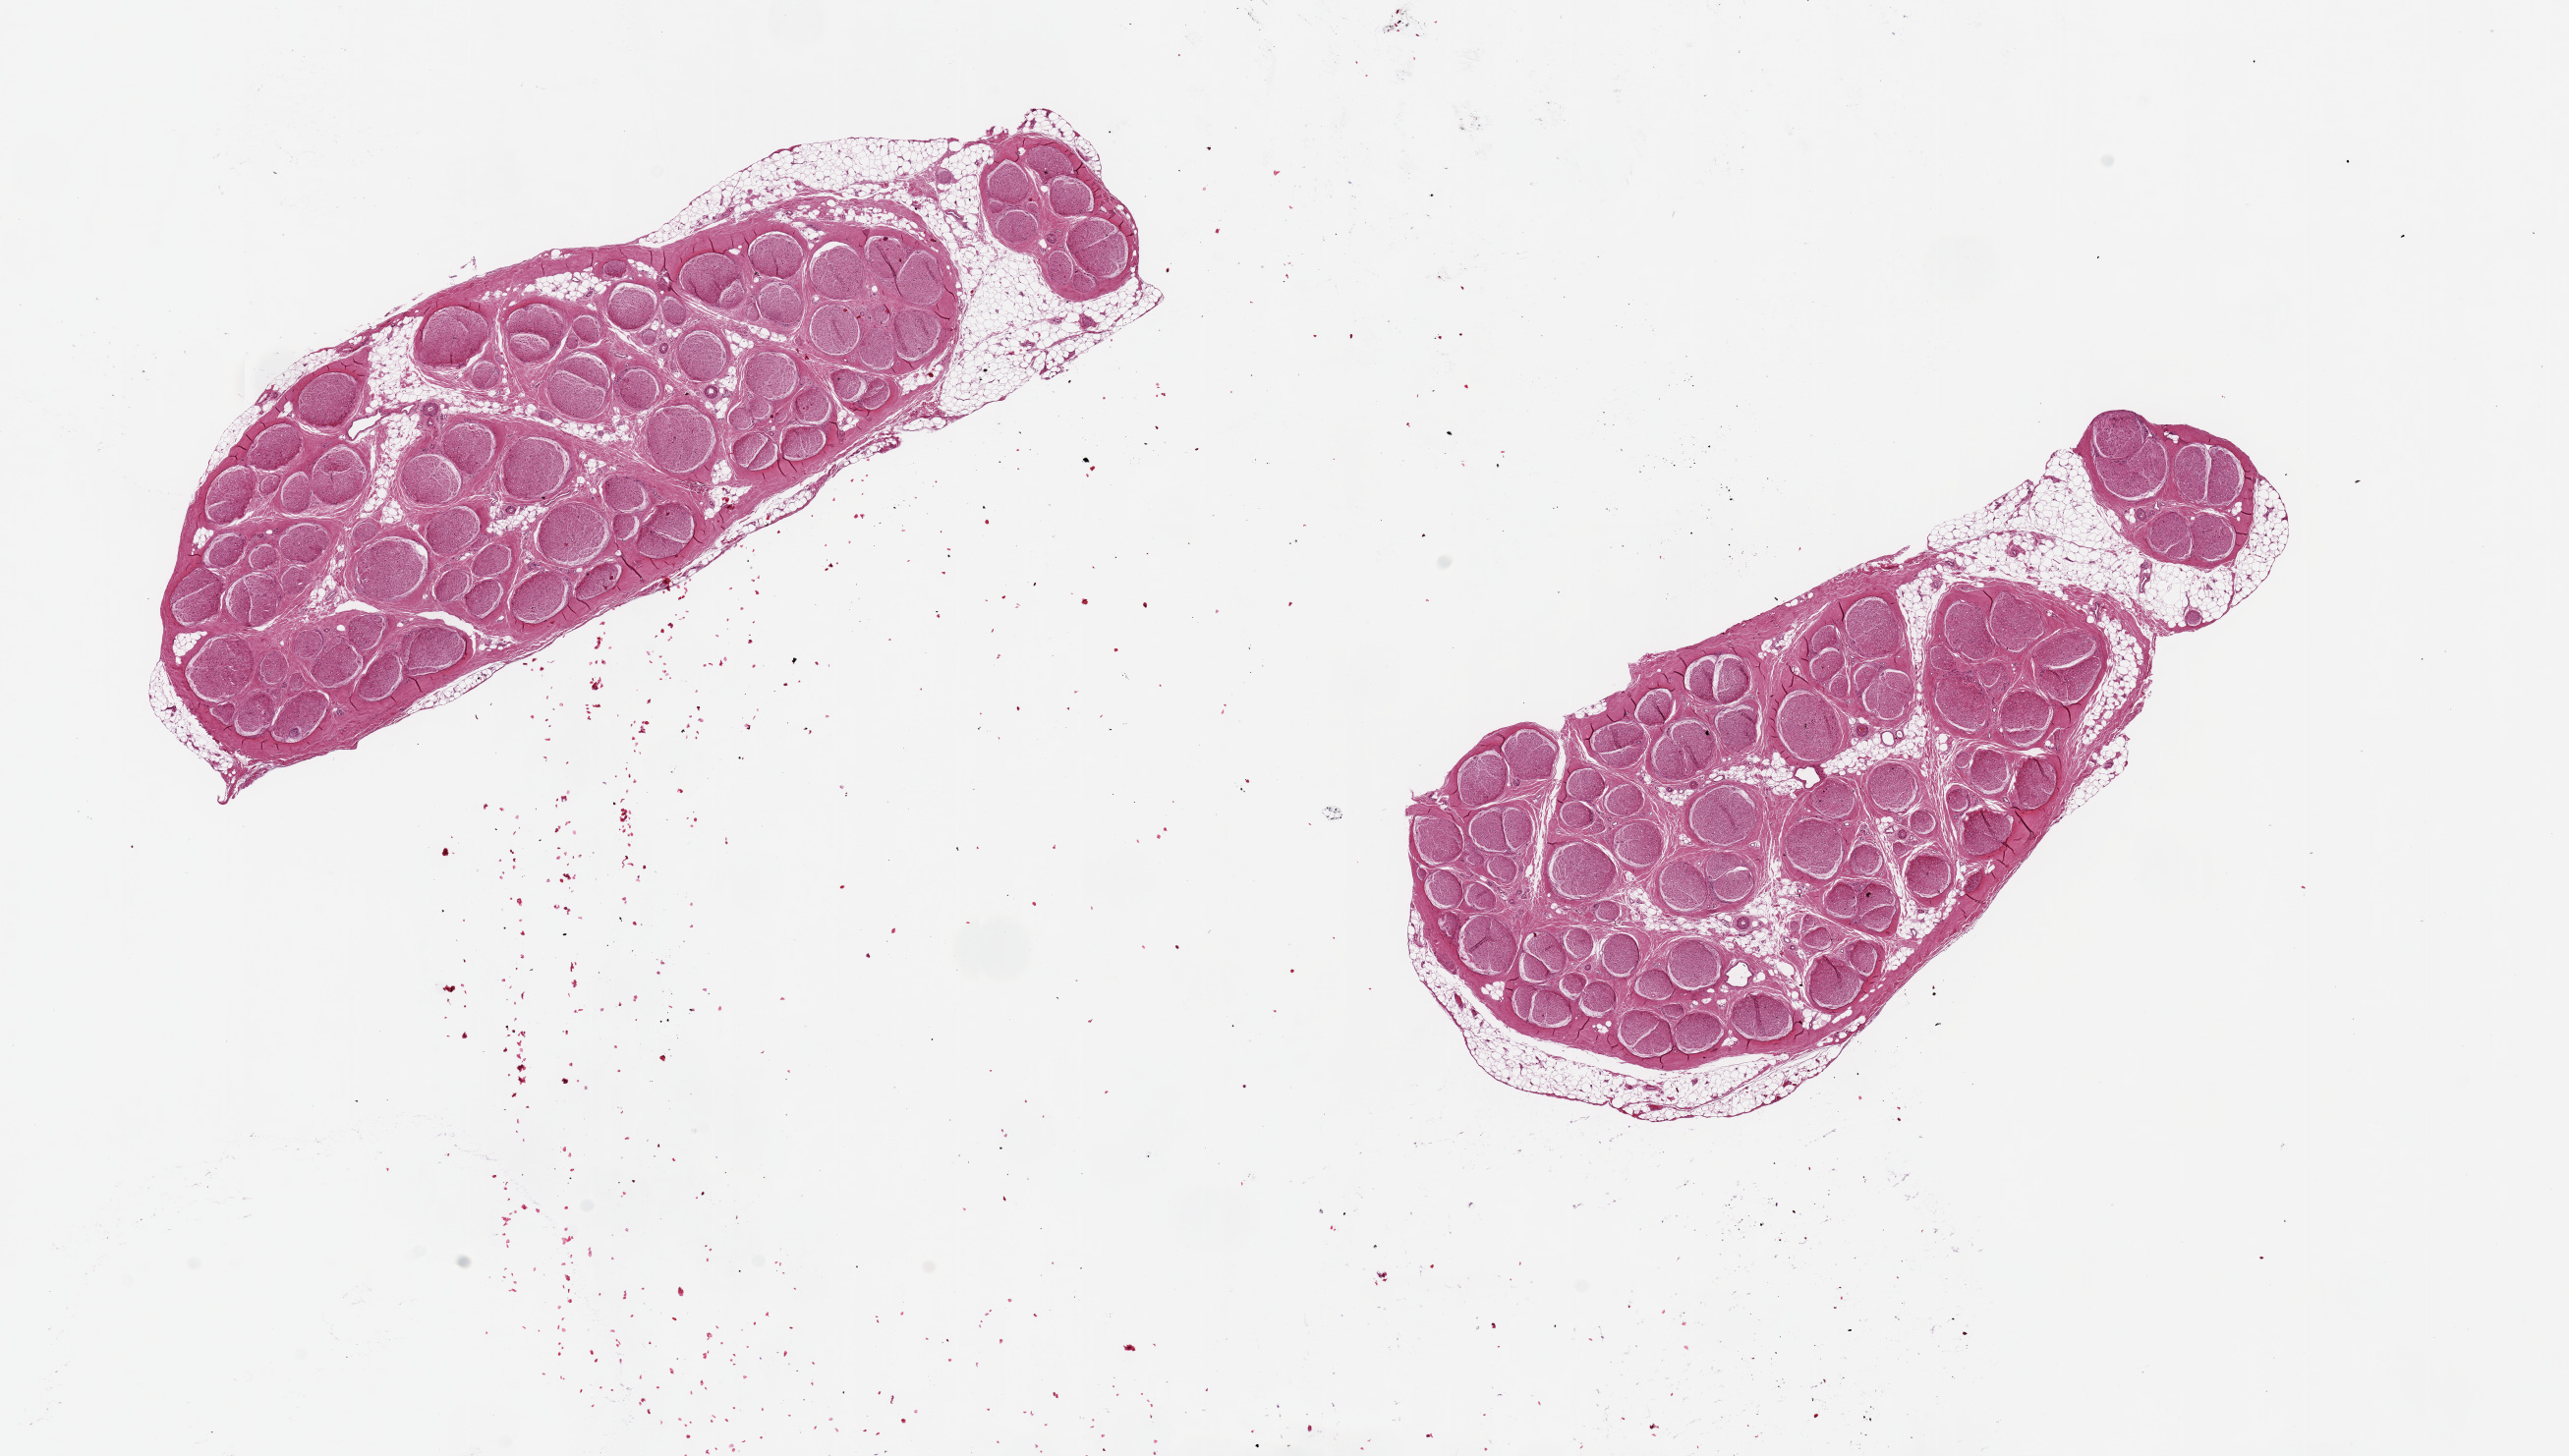
Digitized hematoxylin and eosin (H&E)-stained section, shown as a low-resolution overview of the whole scanned area (about 20.7 x 11.7 mm); PAXgene-fixed paraffin-embedded (PFPE) section; target tissue: tibial nerve; tissue donor sample. Male donor.
- review note (as recorded): 2 pieces ~6x3mm ~10% interstial fat aggregates up to ~1mm in dimension